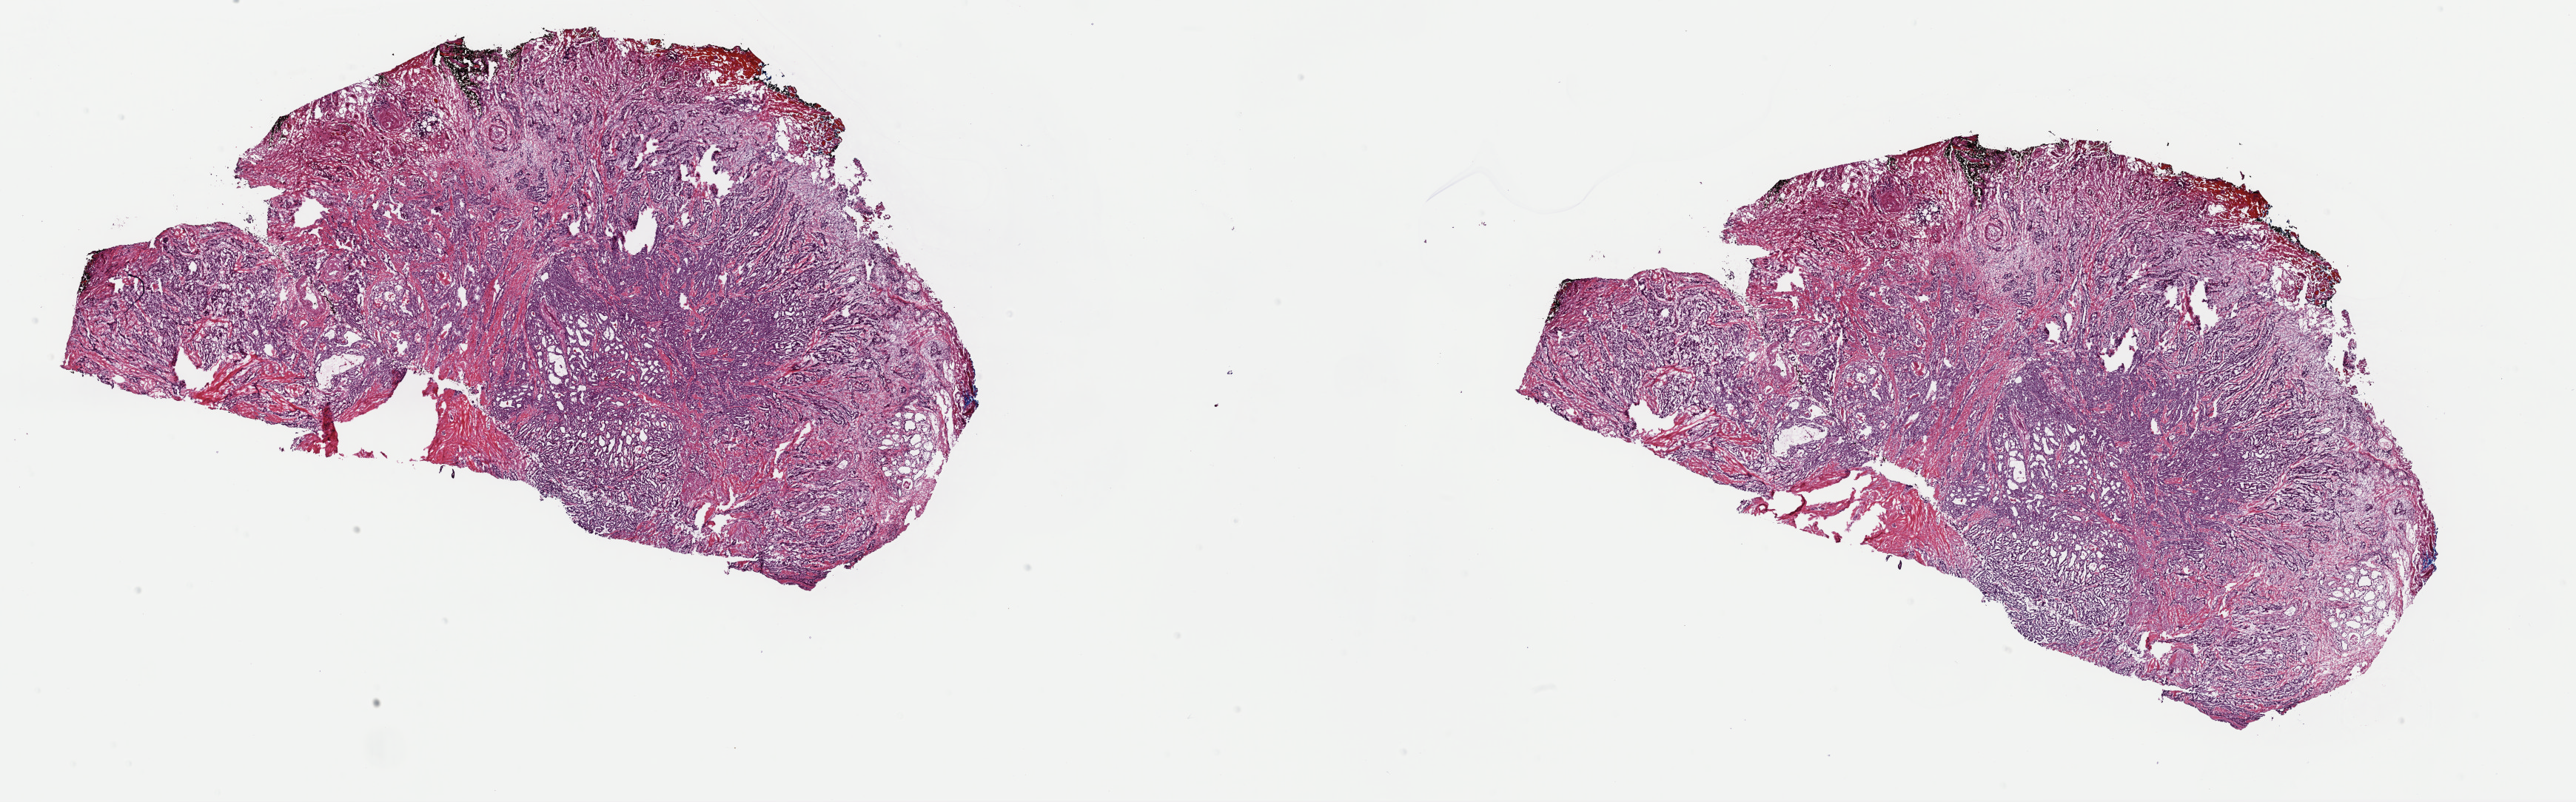
Digitized H&E-stained tissue section (whole slide), low-resolution overview of the scanned area, about 27.5 x 8.6 mm (slide scanned at 40x); frozen section from the top of the tissue portion; thyroid, primary tumour sample. Female patient; age at initial diagnosis 76 years. Pathologist review of this section (percent, as recorded): tumour cells 75%, tumour nuclei 75%, normal cells 3%, stromal cells 22%, necrosis 0%. Inflammatory infiltration, as recorded: lymphocyte infiltration 3%, monocyte infiltration 1%, neutrophil infiltration 1%.
Lymph nodes positive (case pathology): 0 of 1 examined. AJCC pathologic stage: III (7th edition). TNM: T3 N0 M0. Diagnosis: Papillary carcinoma, columnar cell (thyroid gland).